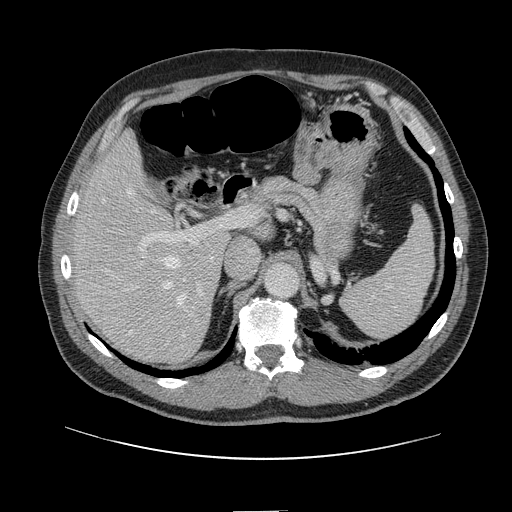
Contrast-enhanced abdominal CT, one axial slice; slice 87 of 161 in the series (ordered by position); soft-tissue window (W 400 / L 40 HU); 512 × 512 image matrix. Male patient, age 66 years. From the clinical record (not read from this slice): diagnosis: colorectal cancer liver metastases, imaged before liver resection; multiple liver metastases: no; largest metastasis: 3.5 cm; disease in both lobes: no.
Outlined on this slice (outlined manually by an expert reader):
- hepatic veins: bounding box <103,187,186,334> (left, top, right, bottom; pixels)
- liver: <76,137,228,362>
- planned liver remnant (the part of the liver to remain after resection): <76,137,170,304>
- portal vein (with intrahepatic branches): <137,214,243,314>